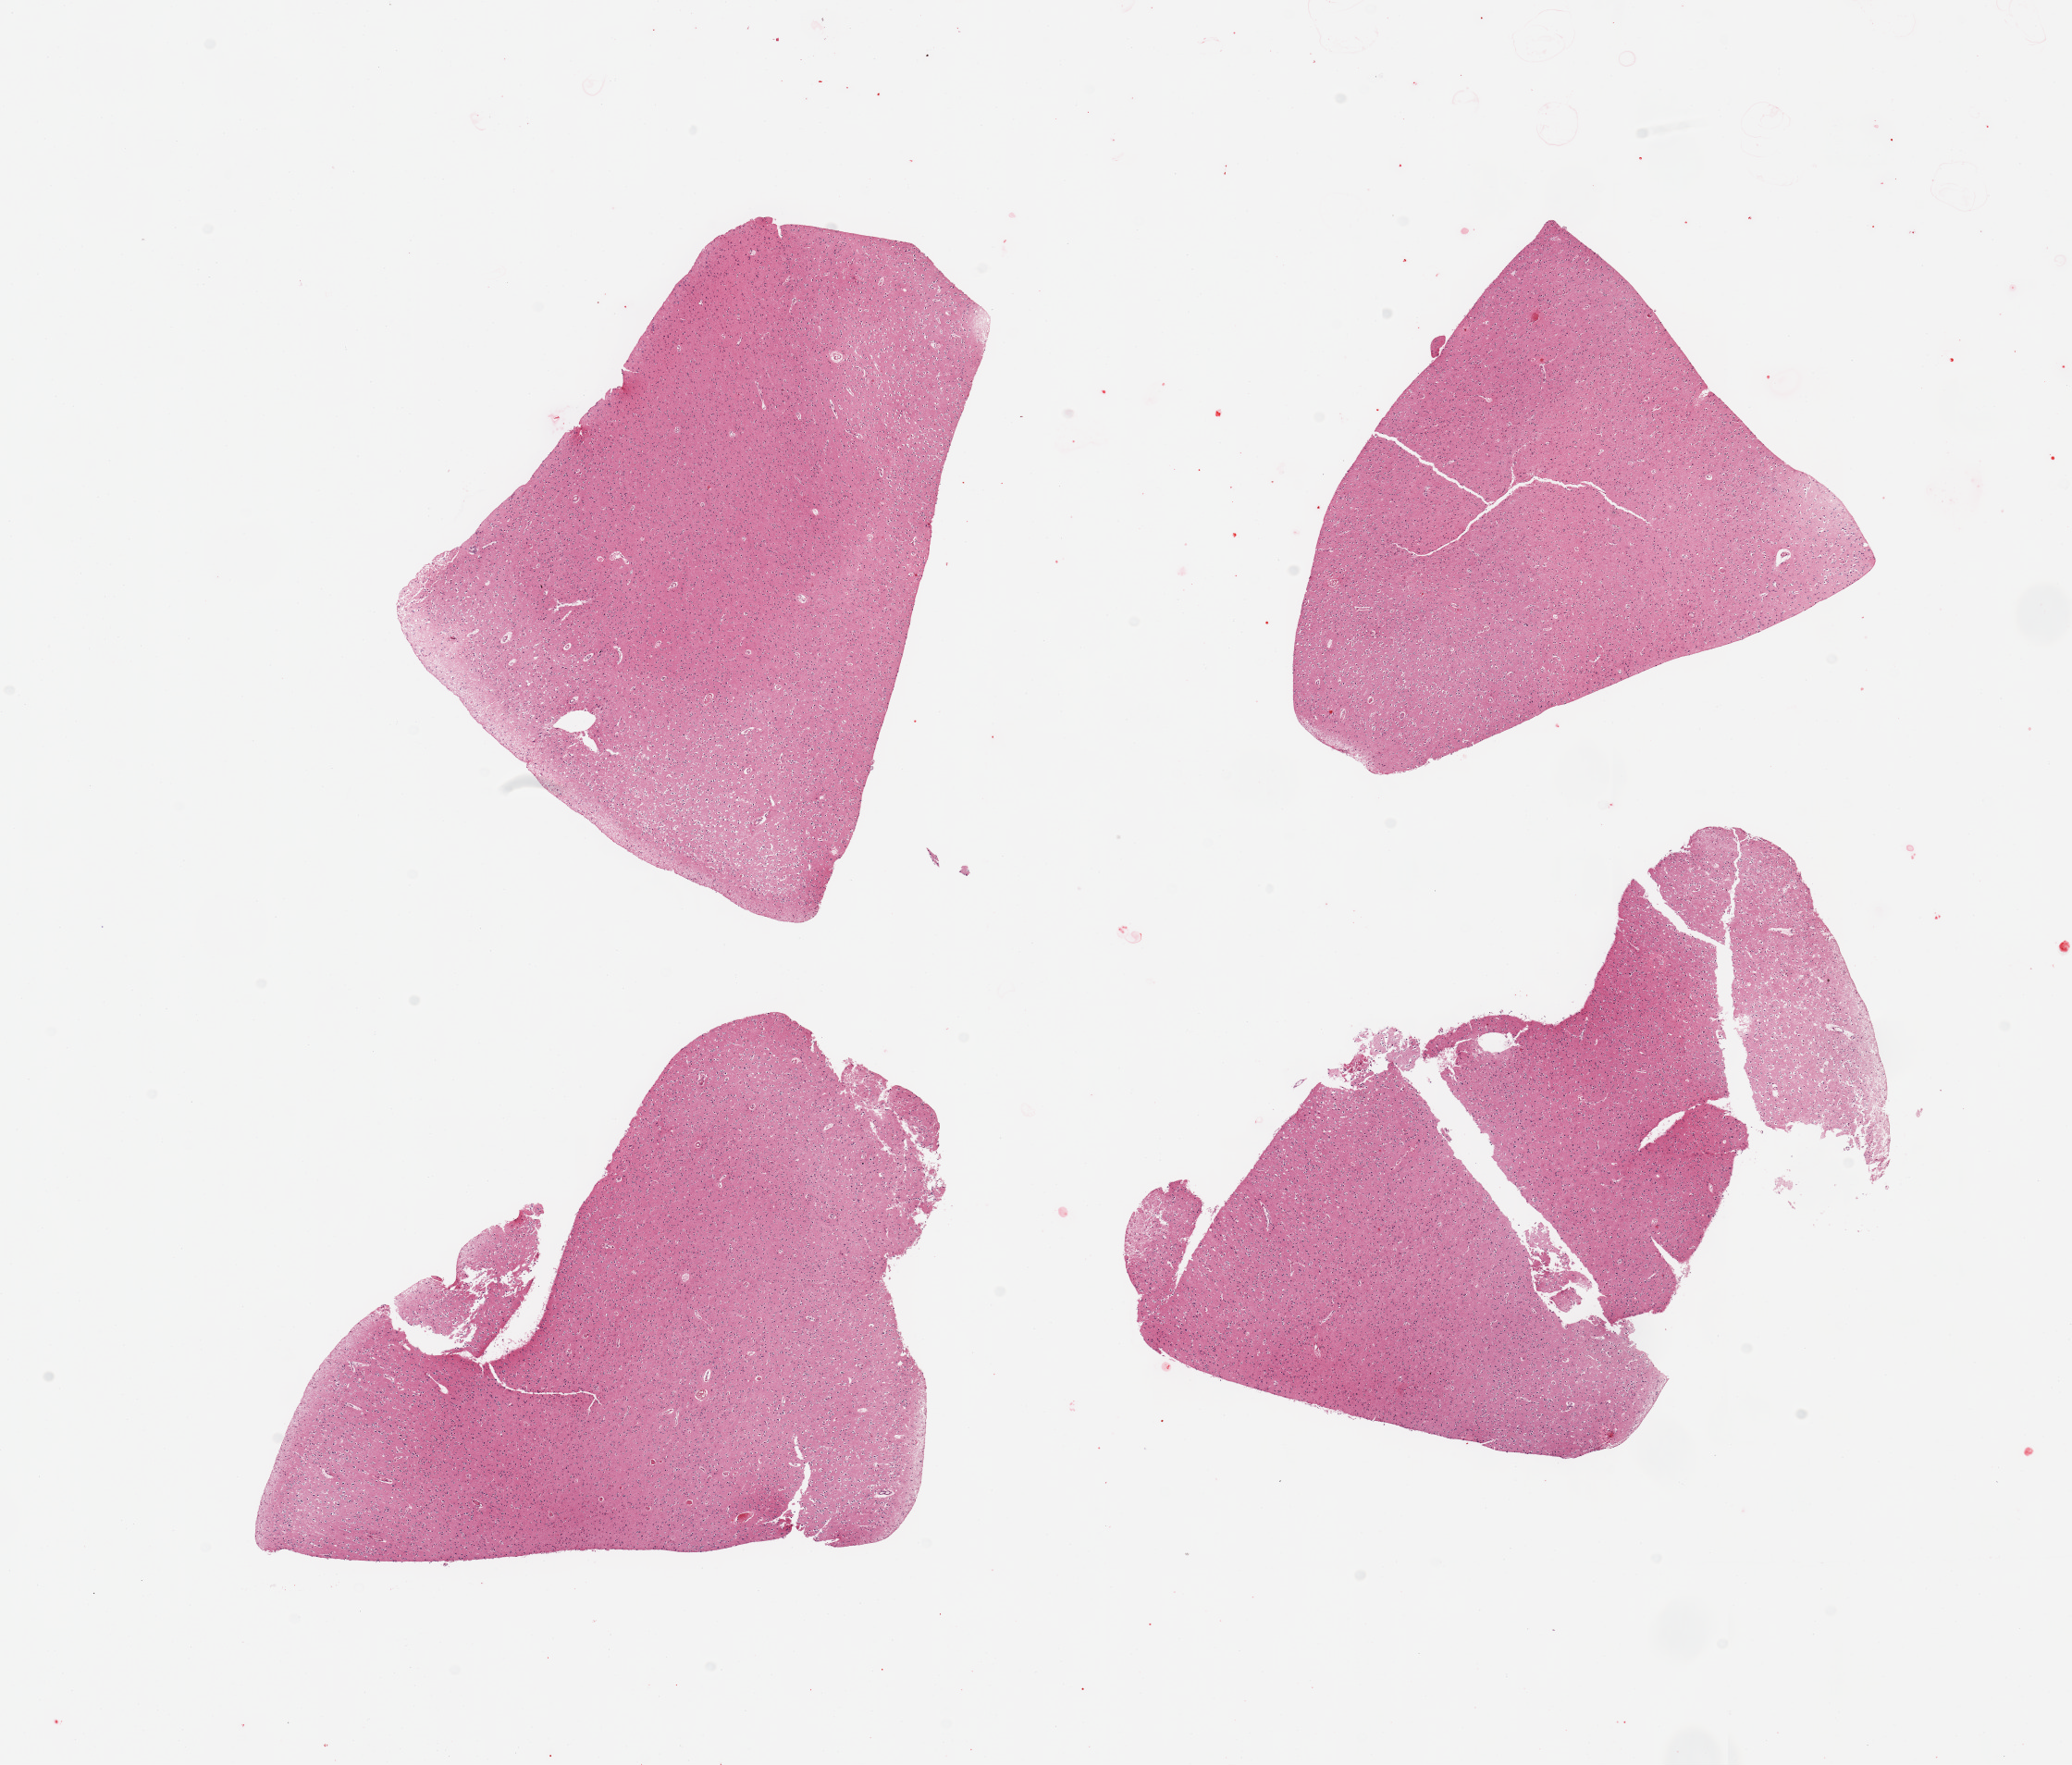
Digitized H&E-stained section, low-resolution overview of the scanned area, about 17.7 x 15.1 mm, PAXgene-fixed paraffin-embedded (PFPE) section, section of cerebral cortex (target tissue), tissue donor sample. Donor sex: female.
Review note (as recorded): 4 pieces.